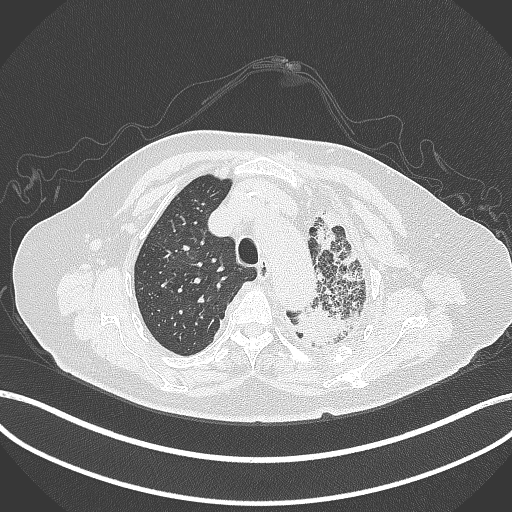
Chest CT, one axial slice; position 307 of 399 along the scan axis; reconstruction kernel B70f; 120 kVp; lung window (W 1500 / L -600 HU); 1 mm slice thickness; 512 × 512 image matrix. Female patient, age 75 years. From the clinical record (not read from this slice): clinical TNM (as recorded): T3 N3 M1.
Annotated regions visible in this slice (bounding box drawn by a radiologist):
- lung tumour (recorded histology: adenocarcinoma): bounding box <287,290,366,350> (left, top, right, bottom; pixels)